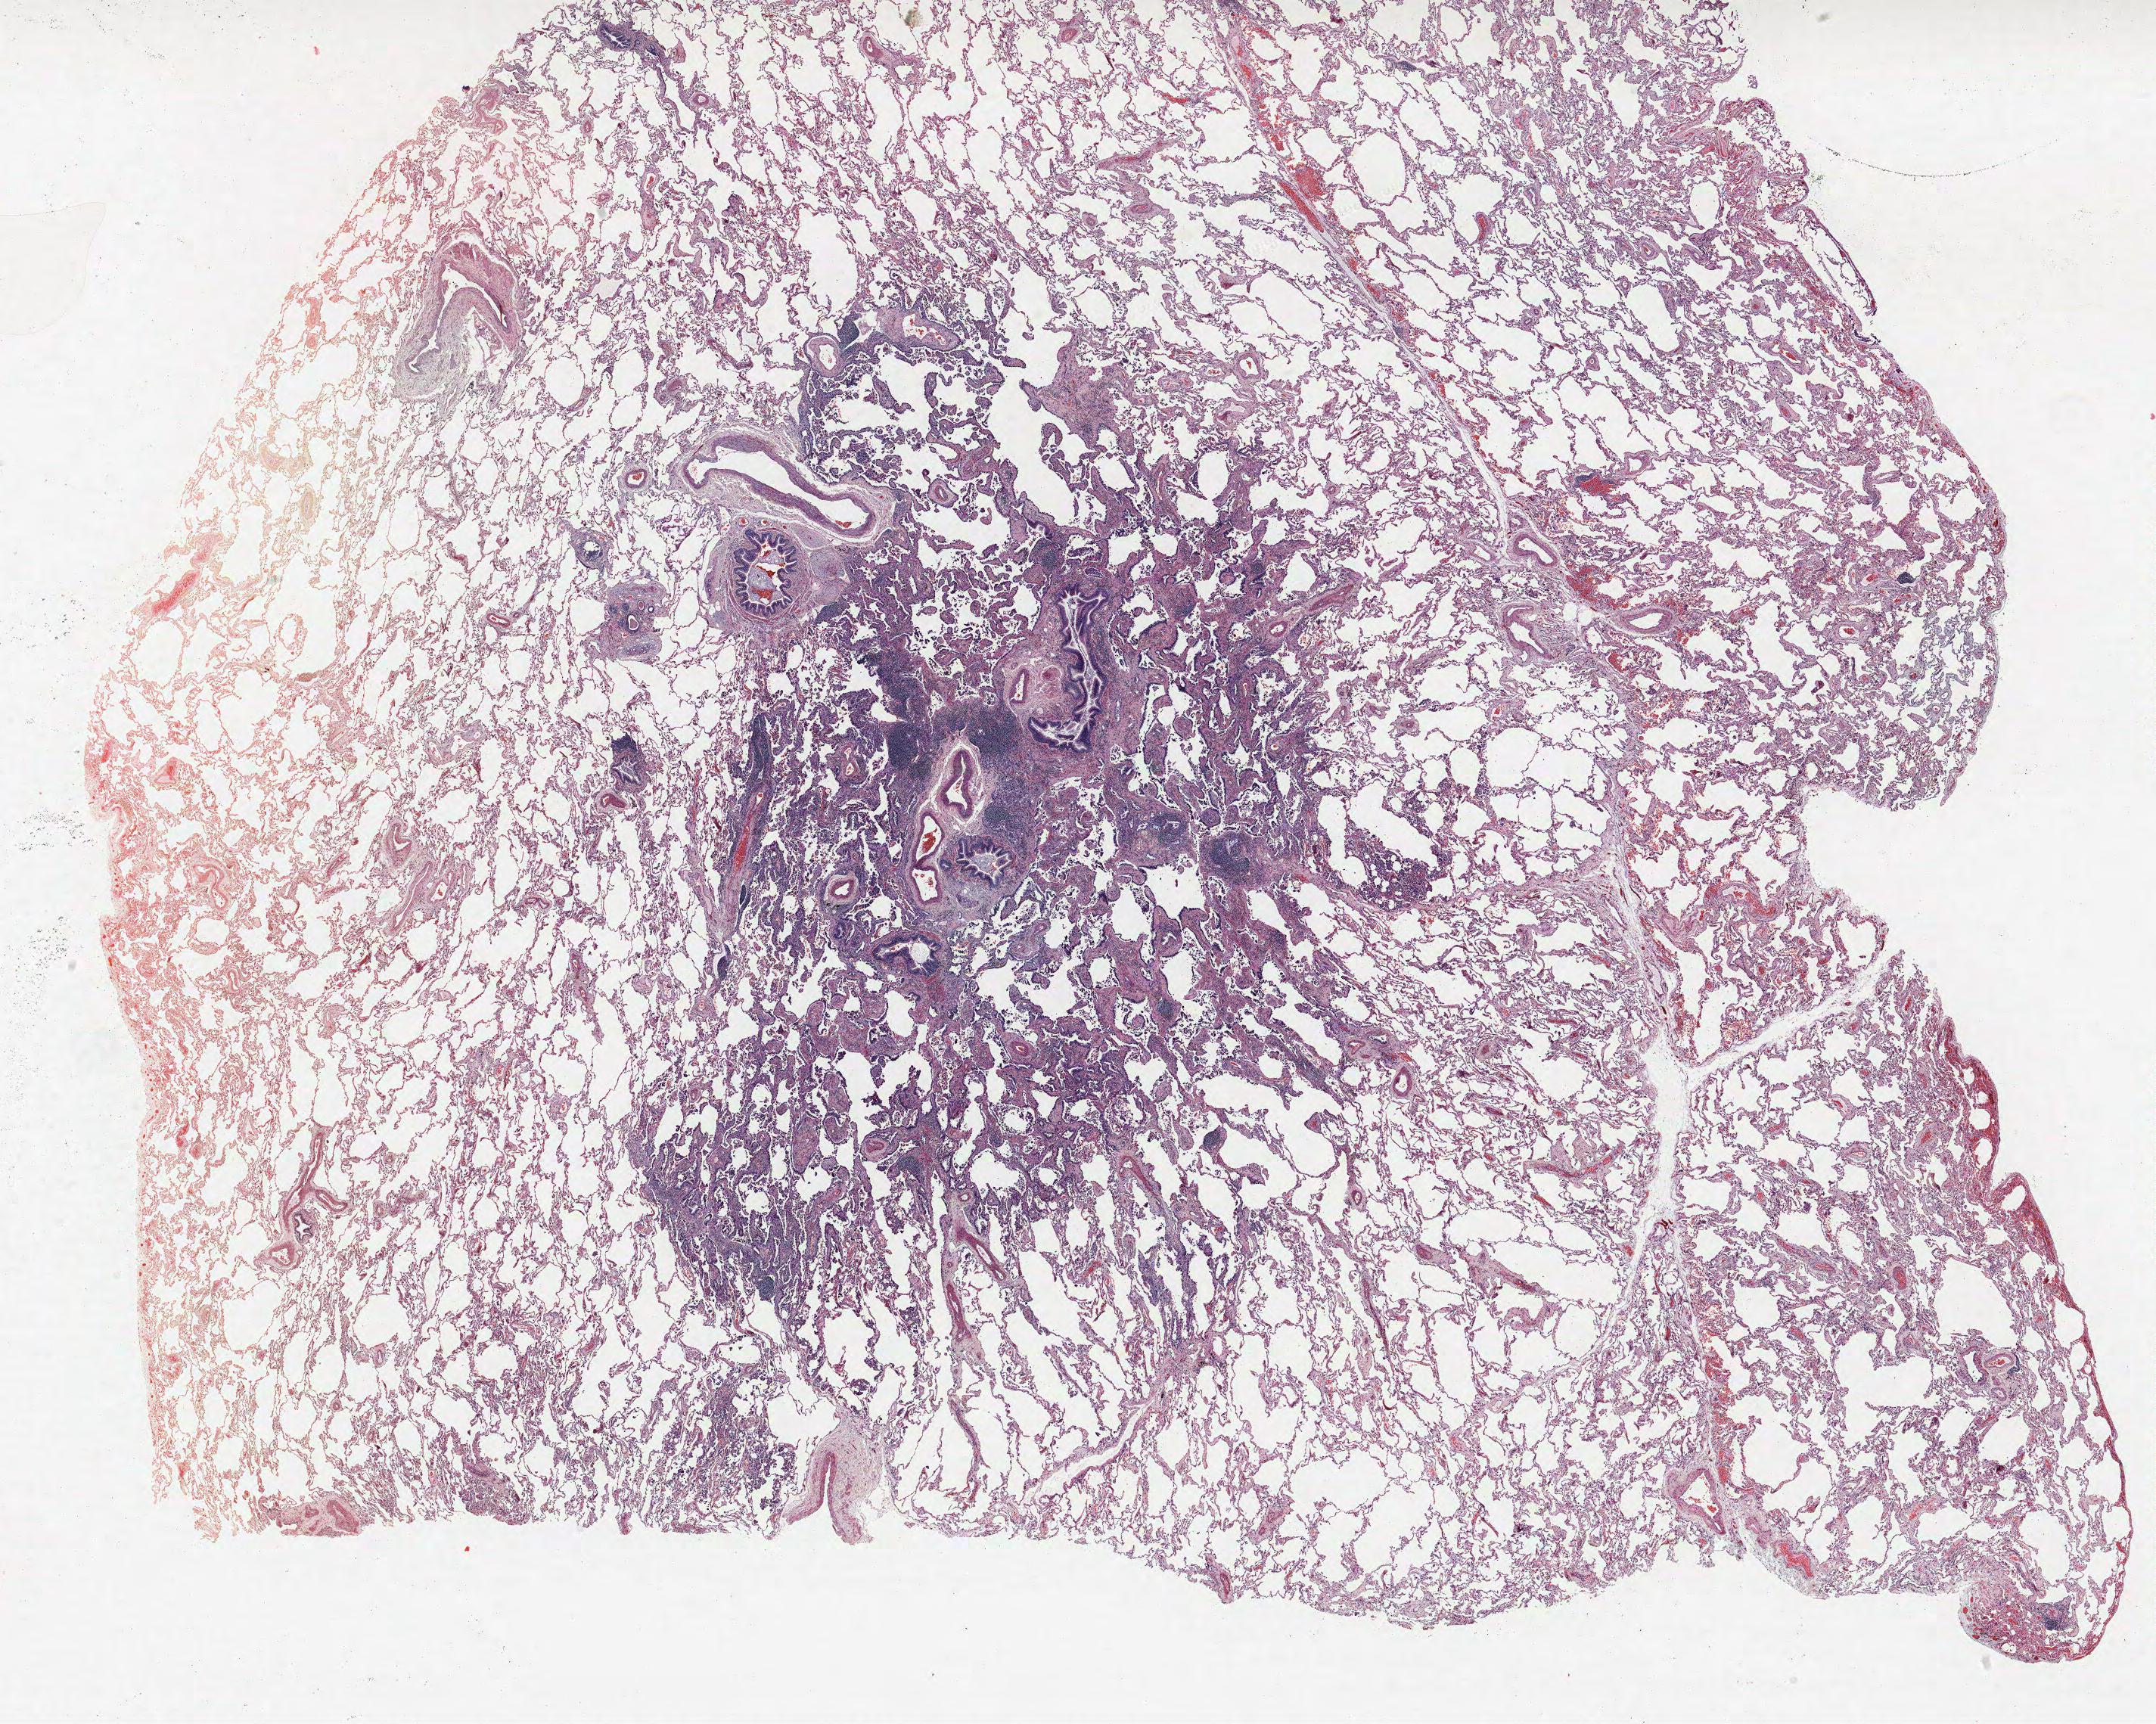
Whole-slide histology image, H&E-stained, shown as a low-resolution overview of the whole scanned area (about 22.8 x 18.2 mm). Formalin-fixed paraffin-embedded (FFPE) section. Lung. Female patient, aged 71 at enrolment. Current smoker at enrolment. Grade: moderately differentiated (G2).
- tumour size (pathology): 12 mm
- primary tumour location (clinical record): right middle lobe
- stage (AJCC 6th edition): IA
- participant's lung-cancer diagnosis: Adenocarcinoma, NOS (ICD-O-3 8140/3)